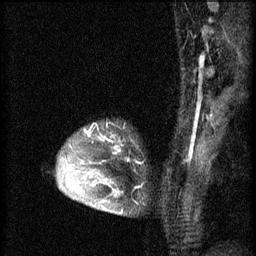
Breast MRI (dynamic contrast-enhanced), one sagittal slice; position 47 of 60 along the scan axis; 3 images stored at this slice position (order not interpretable as contrast timing); 1.5 T; TE 4.2 ms, TR 8.2 ms; 256 × 256 image matrix, field of view 180 × 180 mm. Patient: female, 45 years.
Annotated regions visible in this slice (semi-automatically segmented with operator editing):
- analysis volume of interest (the breast-tissue region the enhancement analysis was run in; not a lesion): bounding box (x1, y1, x2, y2) in pixels: (58, 128, 141, 215)
- tumour enhancement mask (voxels above the 70 % enhancement threshold inside the analysis volume of interest): (70, 130, 123, 215)